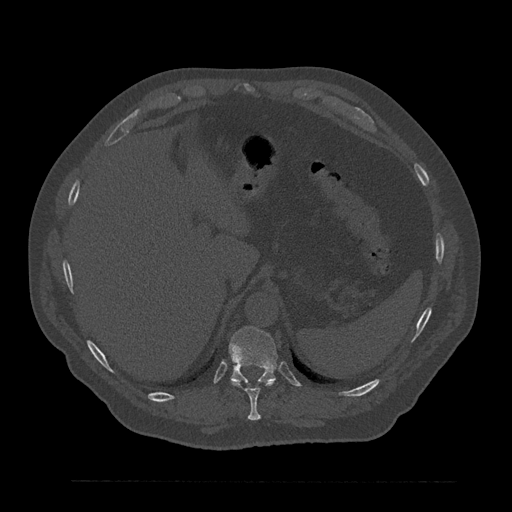
CT including the spine, one axial slice. Slice 321 of 797 in the series (ordered by position). Reconstruction kernel Br40s/3. 120 kVp. Bone window (W 1800 / L 400 HU). 0.5 mm slice thickness. 512 × 512 image matrix, field of view 430 × 430 mm. Patient: male, 61 years. Case-level facts recorded for this patient, not image findings: primary cancer: prostate.
Annotated regions visible in this slice (semi-automatic segmentation, software-assisted and operator-edited):
- T10 vertebra: box from (x=230, y=379) to (x=276, y=421) px
- T11 vertebra: (x=229, y=326)–(x=278, y=384)